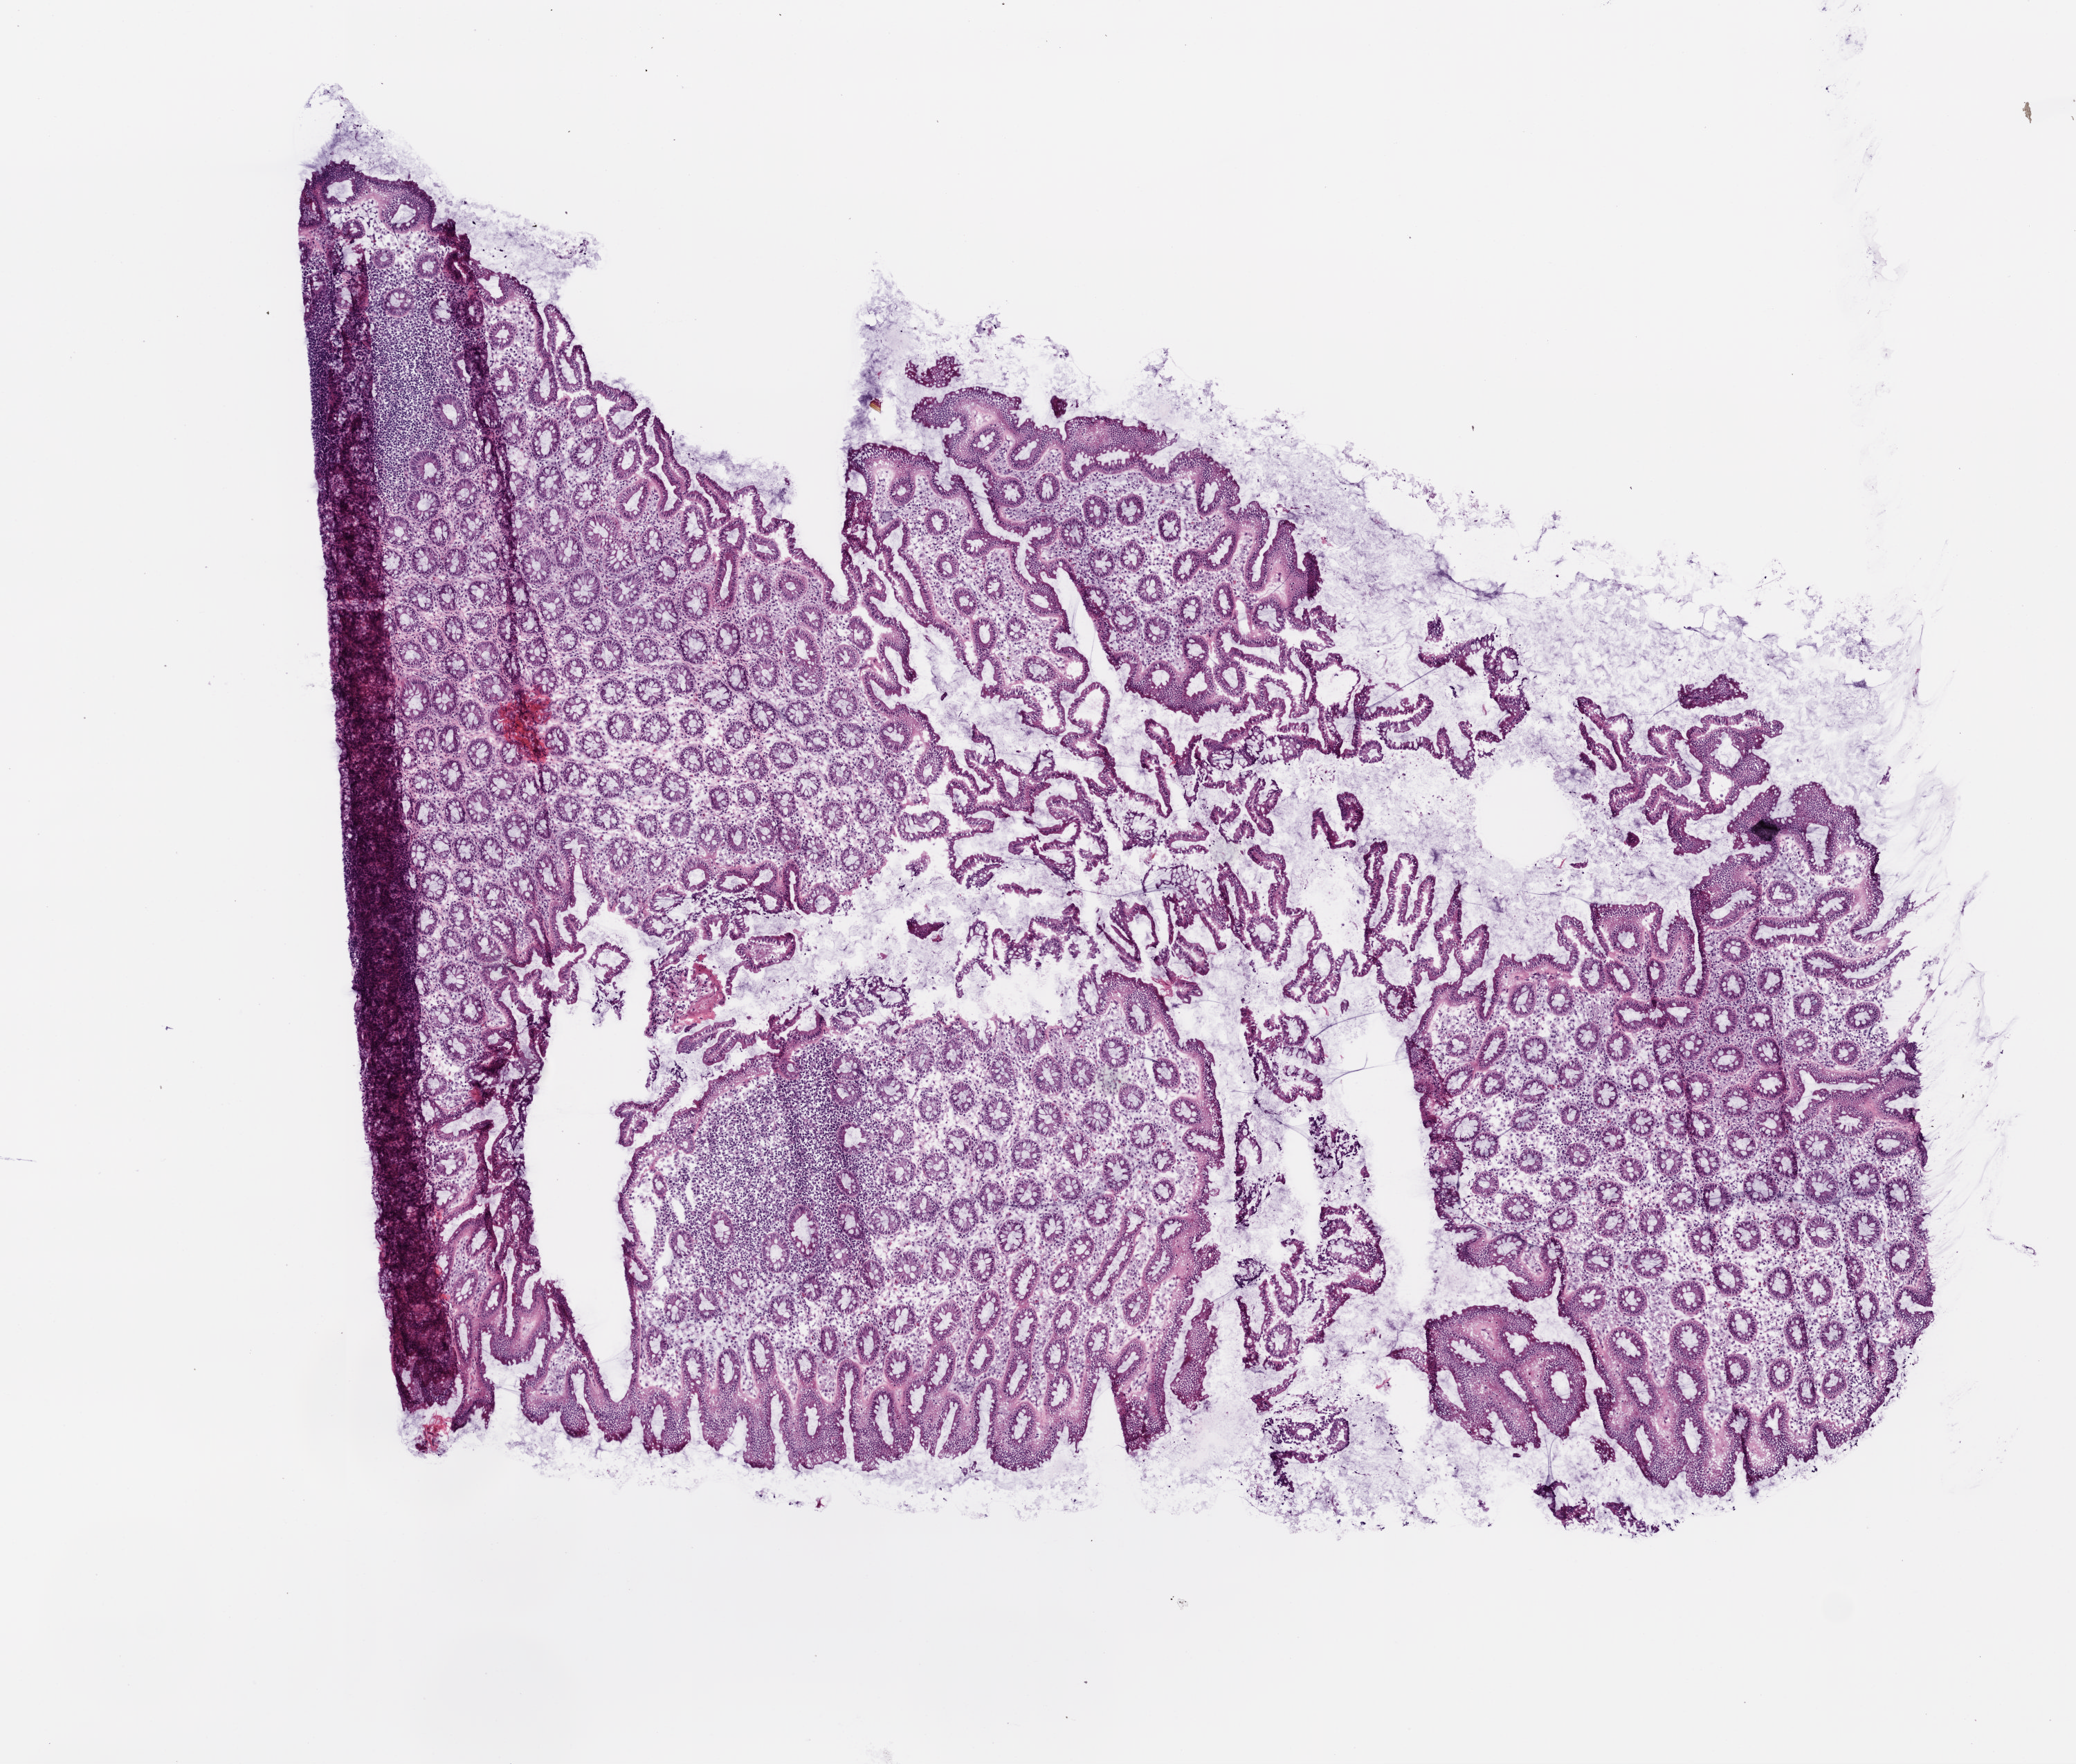
H&E-stained whole-slide image, a low-resolution overview of the entire scanned area, about 6.0 x 5.1 mm (acquisition: 20x scan); frozen section; colon, solid tissue normal (non-tumour tissue) sample. Patient: male, age at initial diagnosis 64 years.
This section: solid tissue normal sample (biorepository sample class). Patient diagnosis: Adenocarcinoma, NOS.